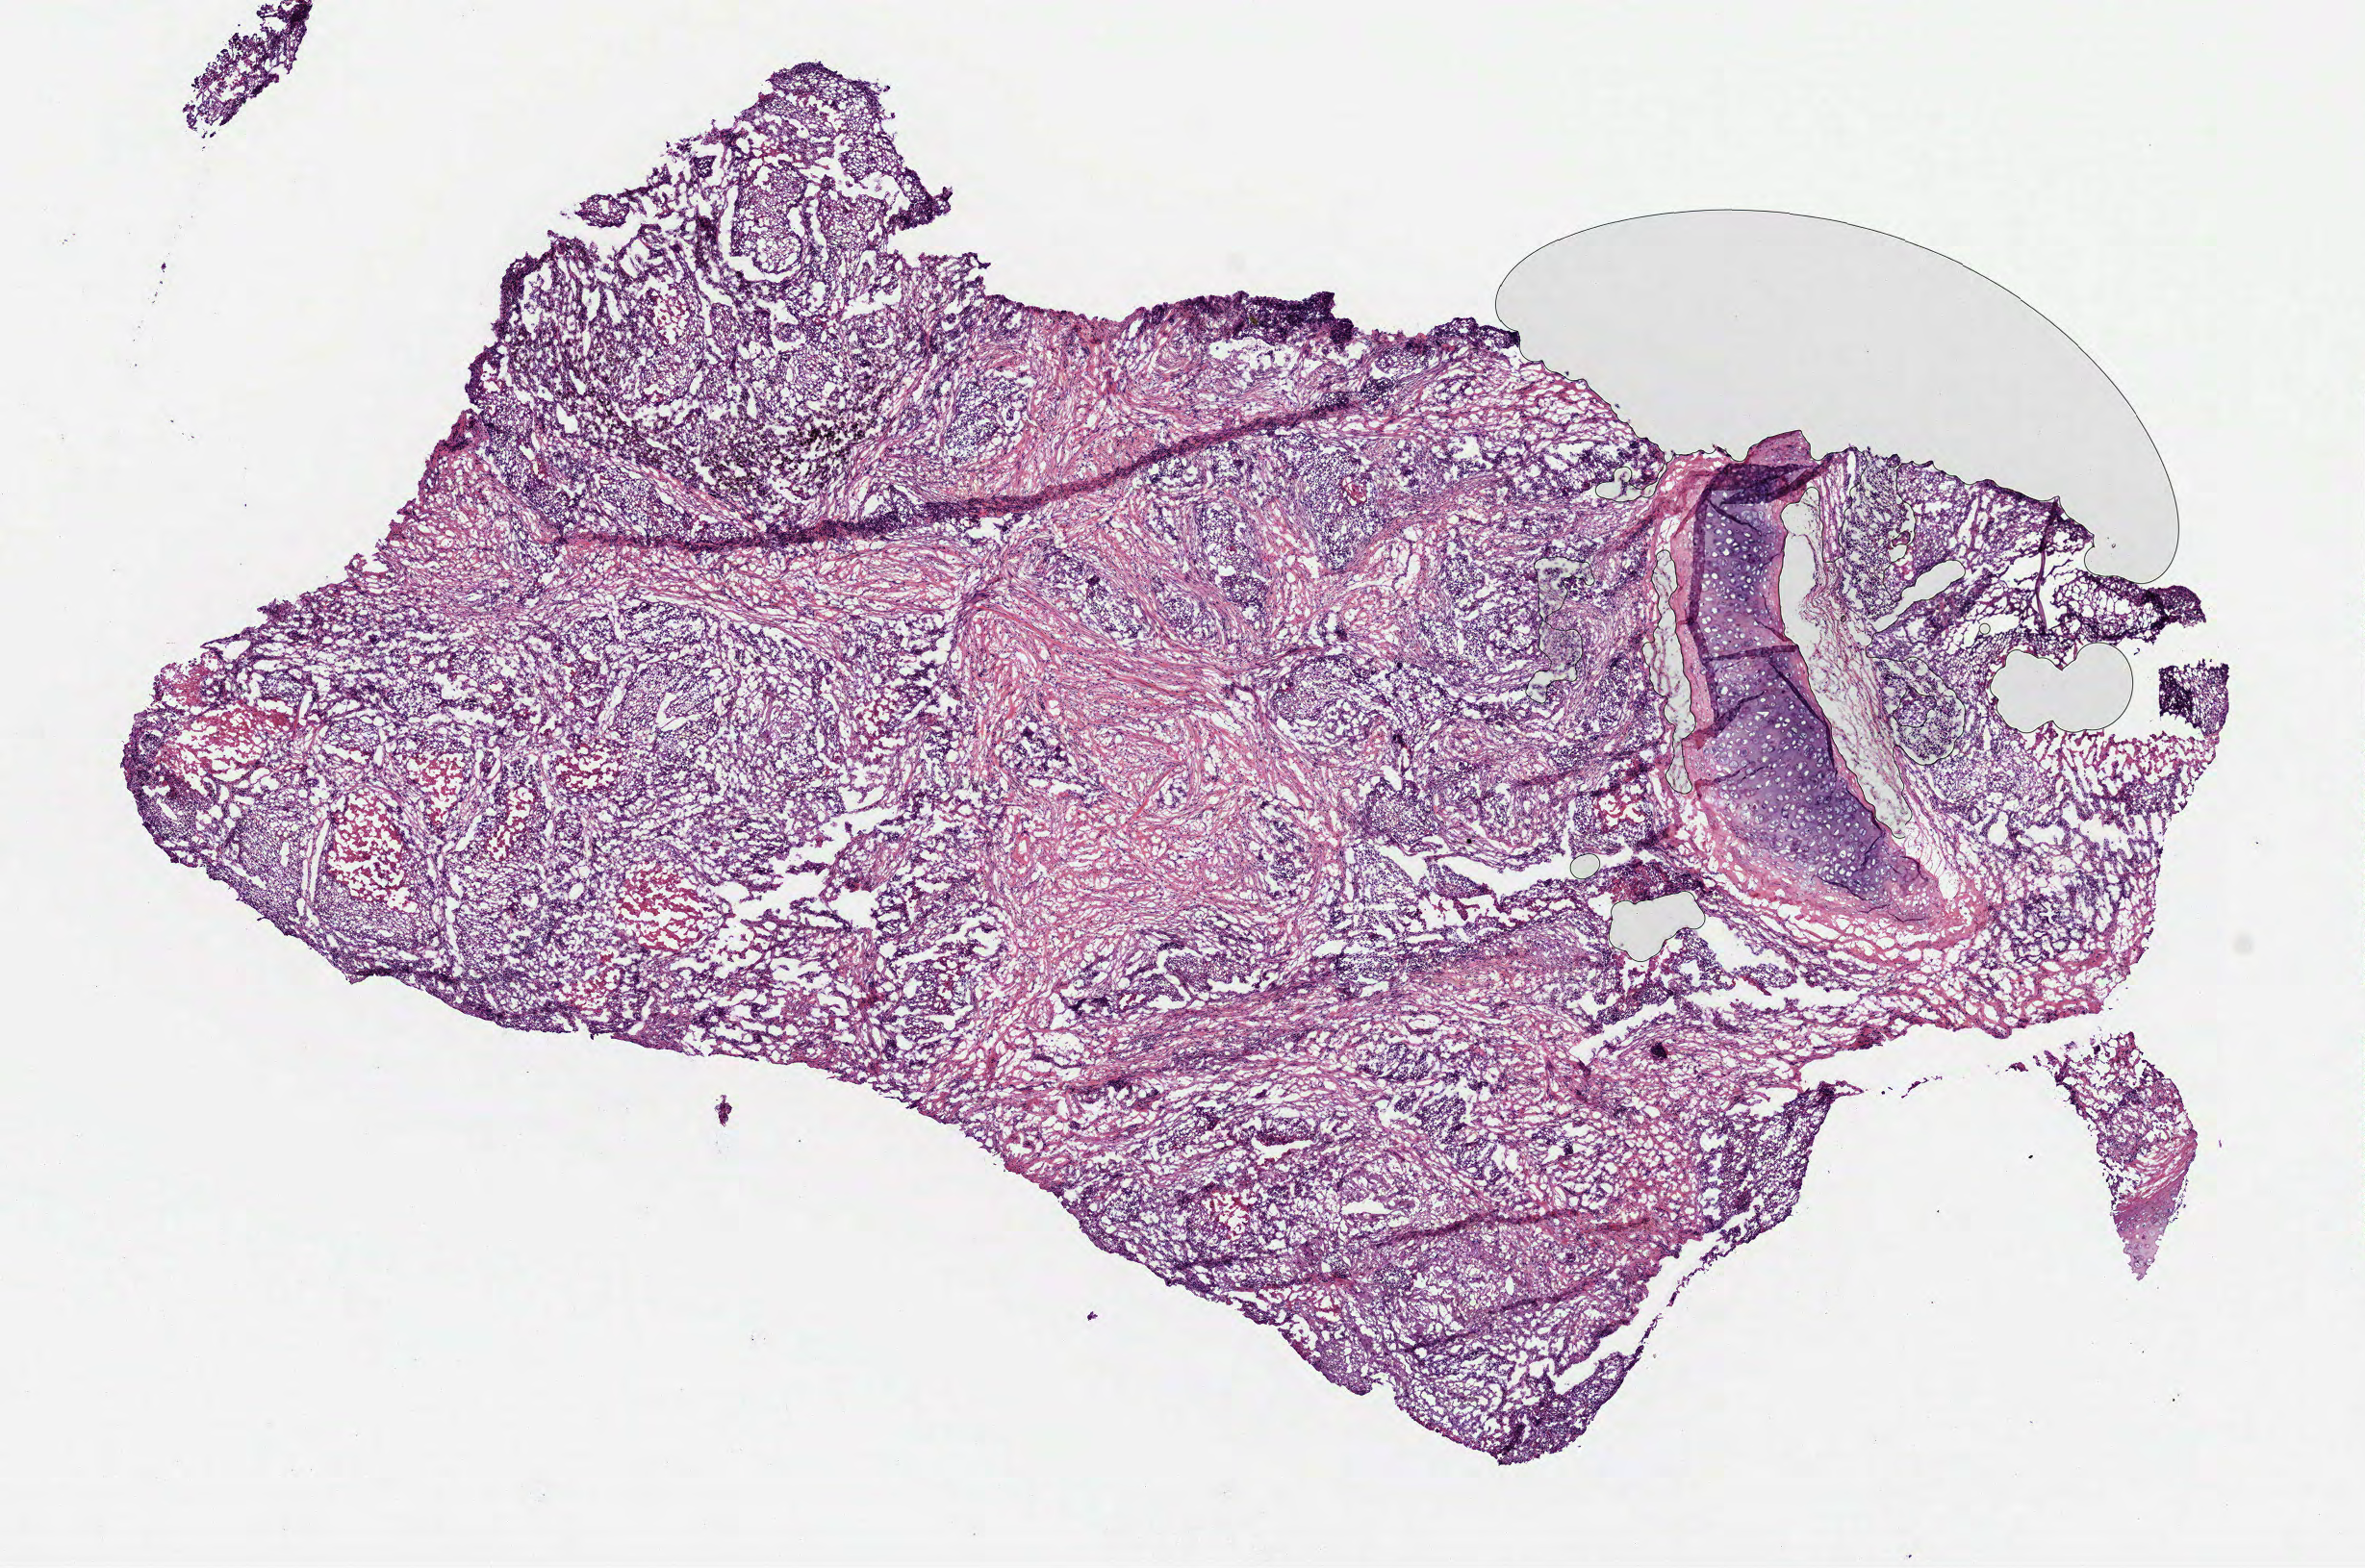
Whole-slide histology image, Hematoxylin and eosin (H&E) stained — whole scanned area (about 9.9 x 6.6 mm, acquisition: 40x scan) shown as a low-resolution overview. Frozen section from the top of the tissue portion. Sample: primary tumour, lung. Patient: female, age at initial diagnosis 62 years. Composition of this section per pathologist review: tumour cells 75%, tumour nuclei 60%, normal cells 11%, stromal cells 11%, necrosis 3%. Infiltration values recorded for this section: lymphocyte infiltration 10%, monocyte infiltration 20%, neutrophil infiltration 1%.
• TNM: T4 N2 M0
• AJCC pathologic stage: IIIB (6th edition)
• histologic diagnosis: Squamous cell carcinoma, keratinizing, NOS